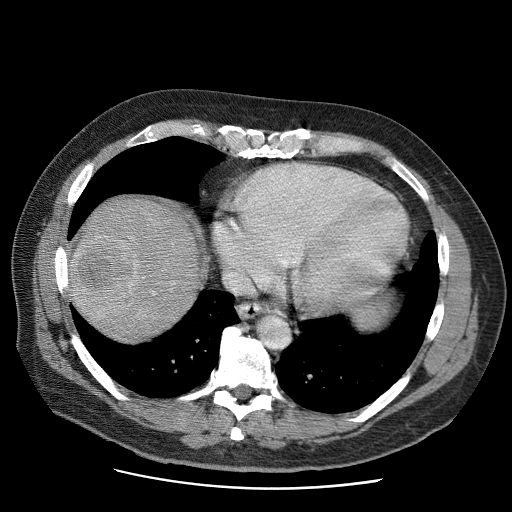
Contrast-enhanced abdominal CT (liver protocol), one axial slice. Position 59 of 81 along the scan axis. 120 kVp. Soft-tissue window (W 400 / L 40 HU). 2.5 mm slice thickness. 512 × 512 image matrix. From the clinical record (not read from this slice): diagnosis: hepatocellular carcinoma (patient treated with transarterial chemoembolisation; whether this scan precedes or follows treatment is not stated here); TNM stage (as recorded): Stage-IIIA; Child-Pugh class: A; tumour differentiation: moderately differentiated; tumour nodularity: multinodular.
Outlined on this slice (semi-automatically segmented with operator editing):
- liver parenchyma outside the tumour (the mass and vessels are separate outlines, so this box may not span the whole liver): bounding box <68,196,204,340> (left, top, right, bottom; pixels)
- mass: <69,227,140,317>